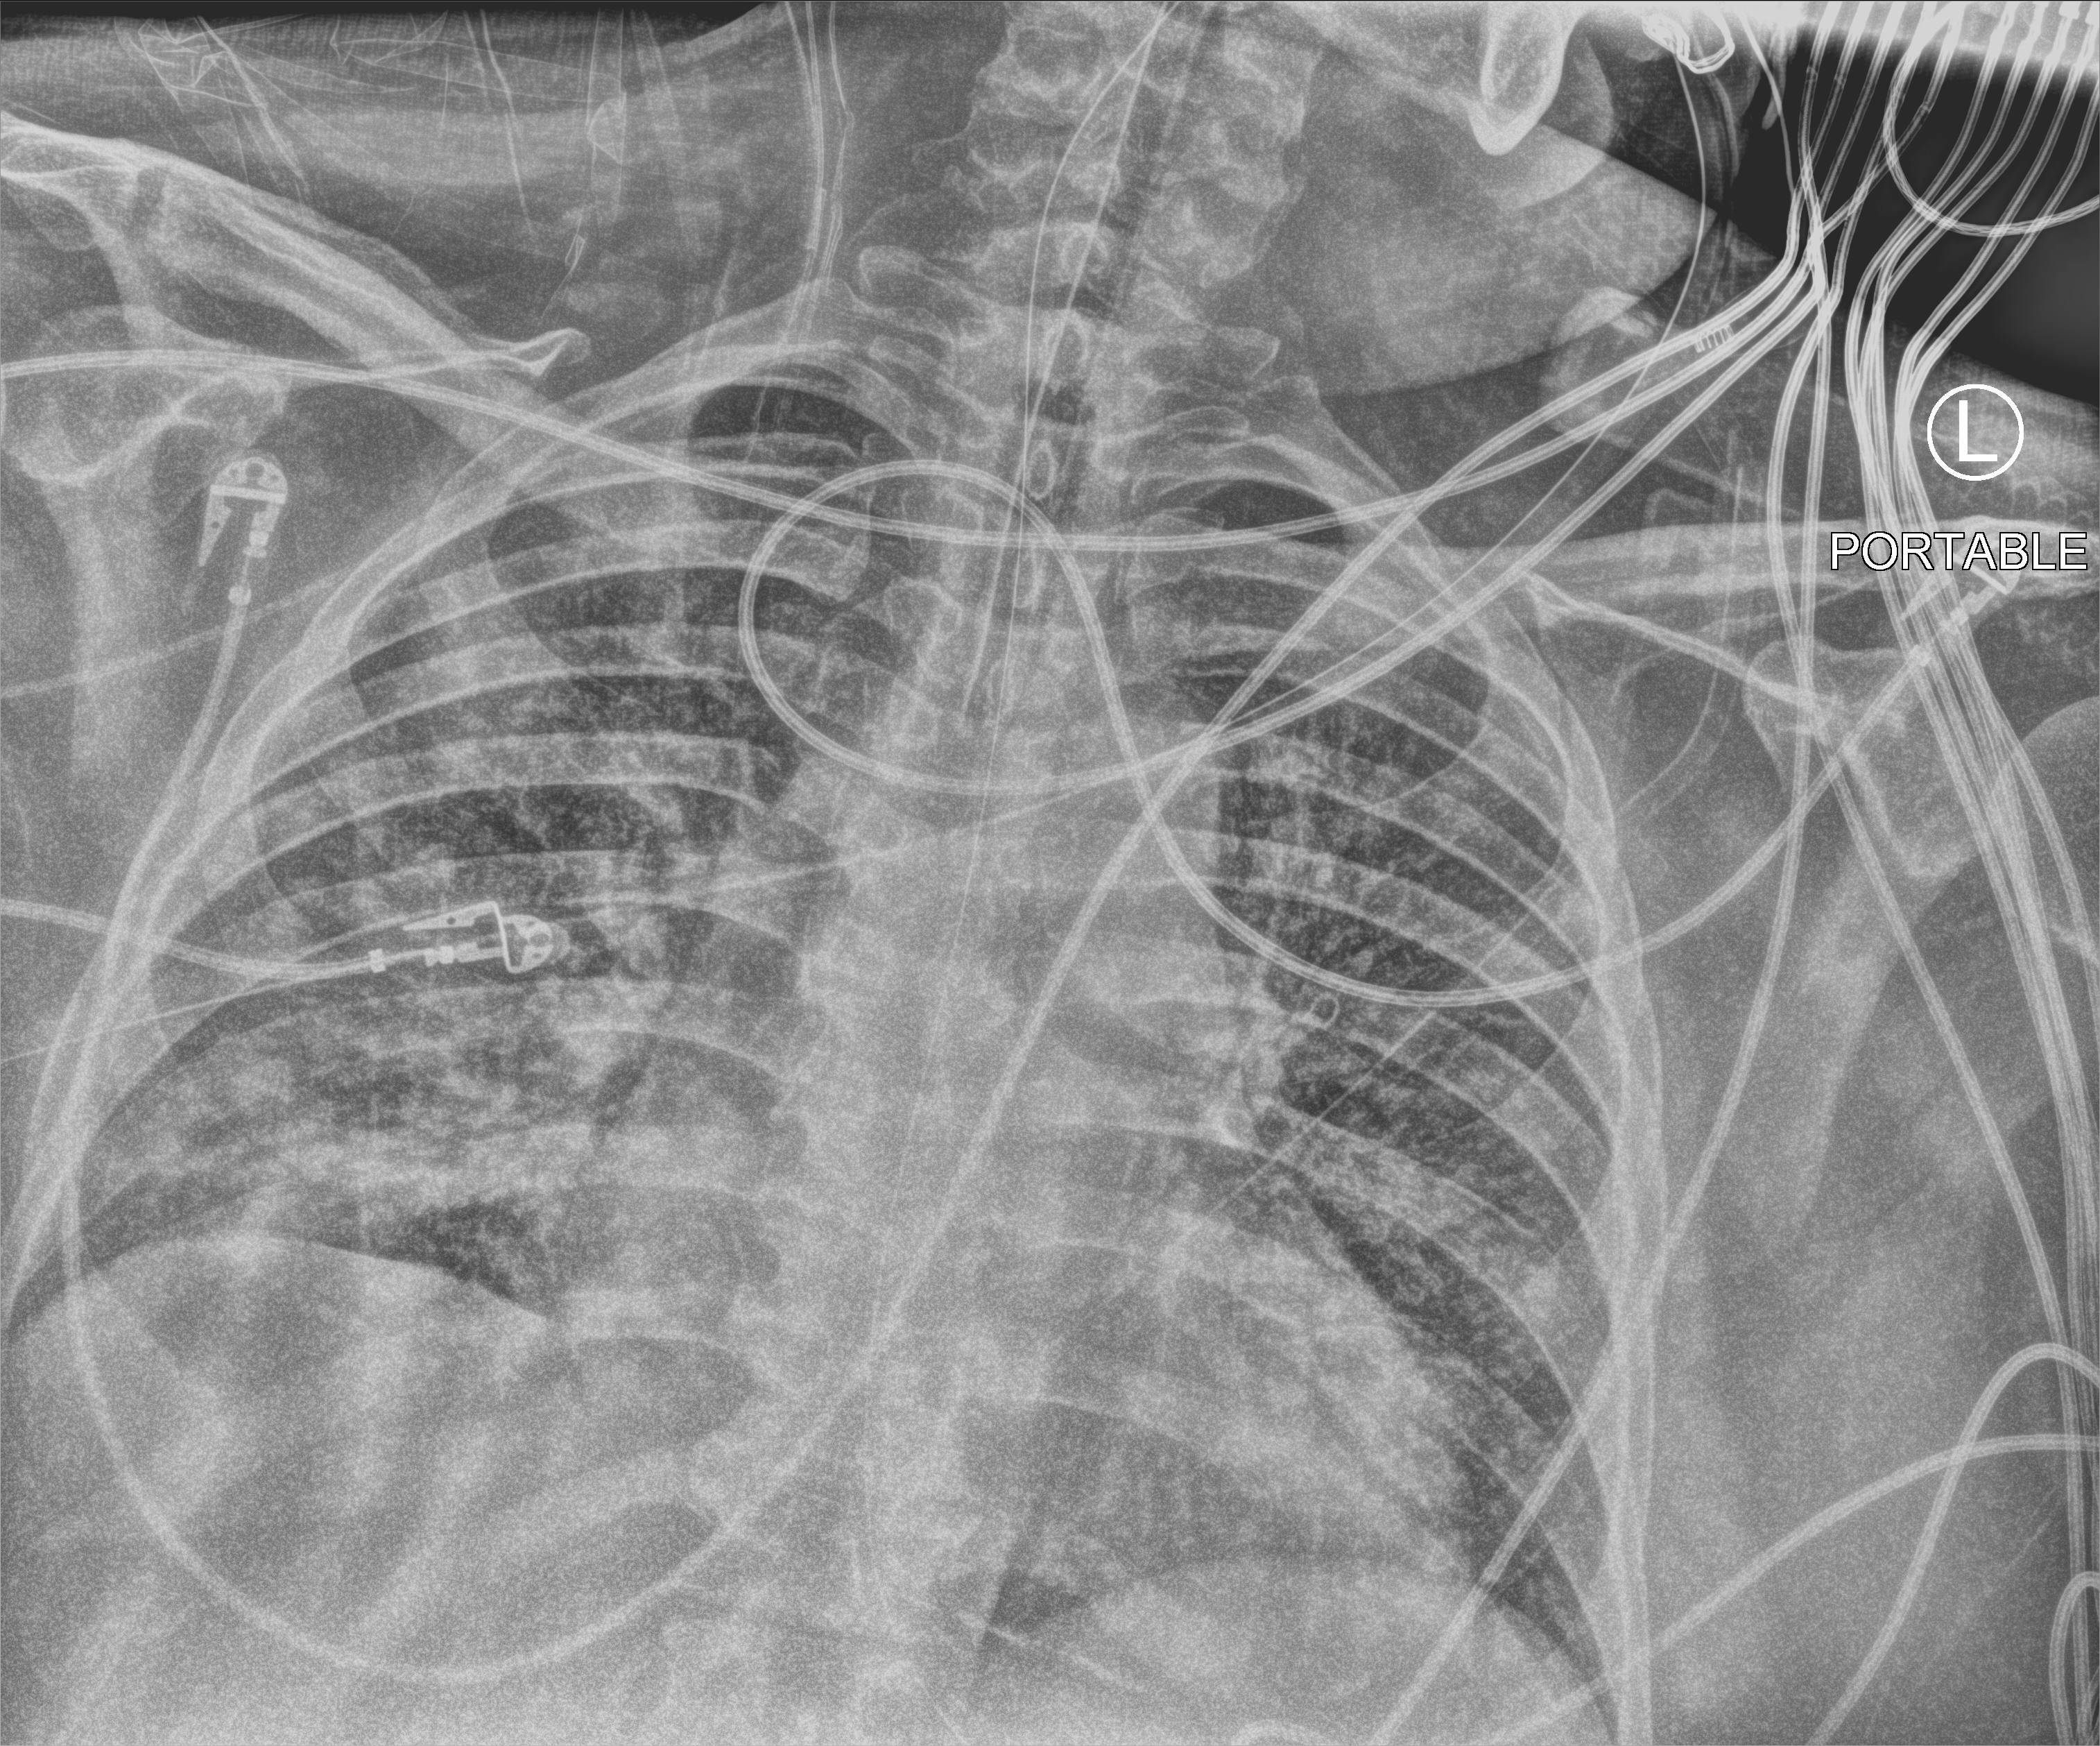
Portable chest radiograph, anteroposterior (AP) projection. Male patient hospitalised with COVID-19, age 18–59 years.
Hospital-stay facts (about this admission, not read from this image; timing relative to this image not recorded):
- admitted to intensive care during this hospital stay: yes
- mechanically ventilated during this hospital stay: yes